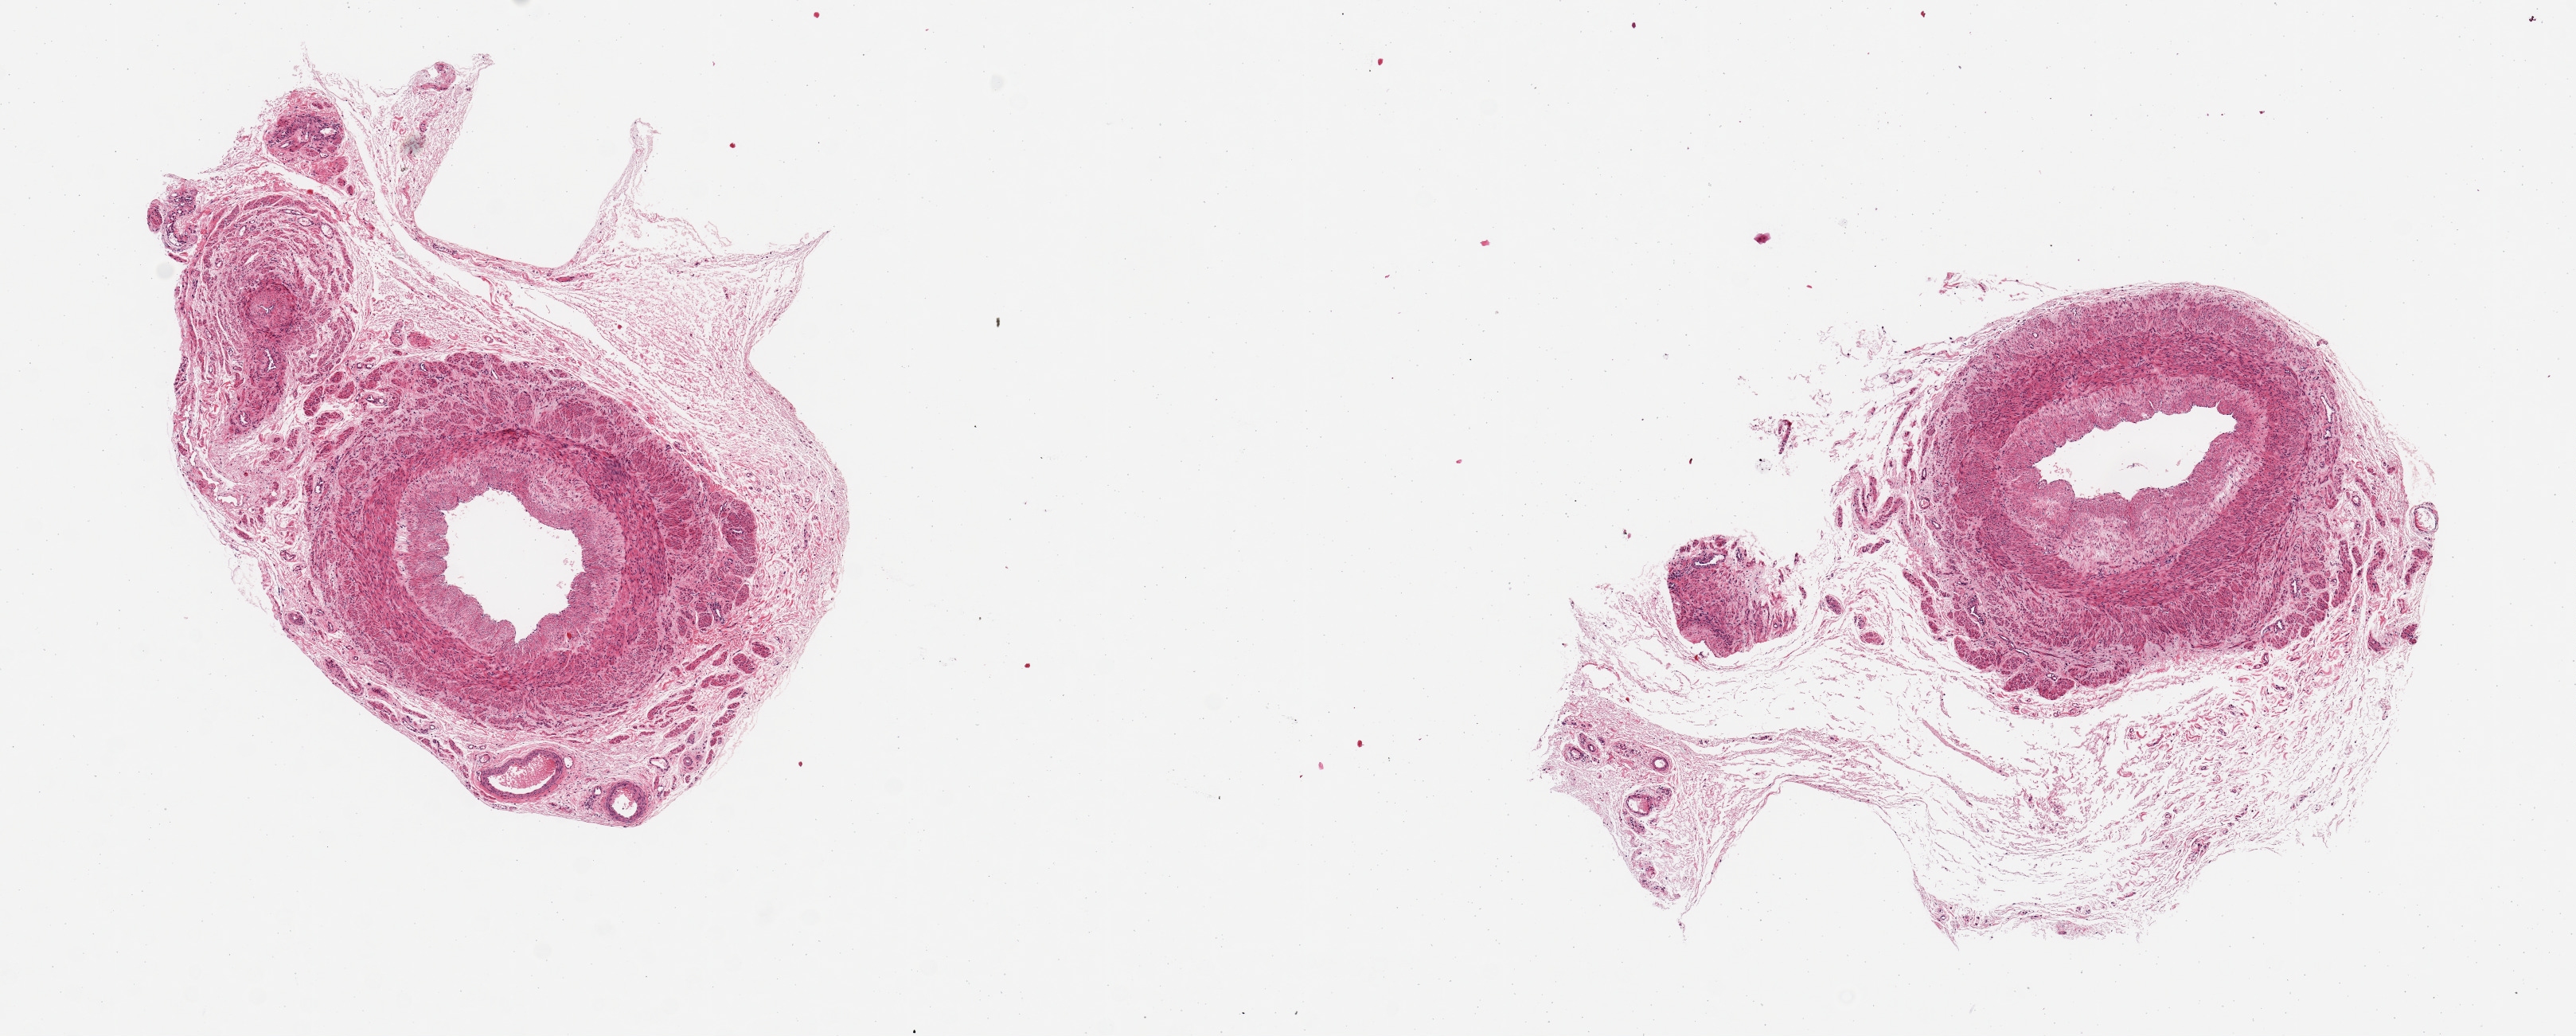
Hematoxylin and eosin (H&E) whole-slide image — shown as a low-resolution overview of the whole scanned area (about 12.8 x 5.1 mm, from a 20x scan); PAXgene-fixed paraffin-embedded (PFPE) section; section of fallopian tube (target tissue); donor tissue sample. Female donor.
Pathologist's review note for this sample: 2 aliquots, artery, not fallopian tube. Unknown provenance.